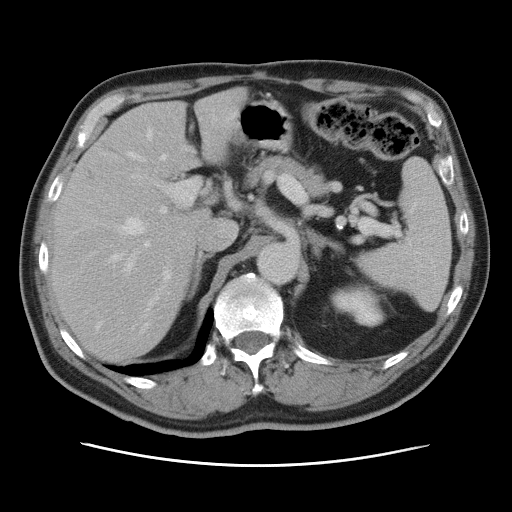
Contrast-enhanced abdominal CT, one axial slice. Position 51 of 80 along the scan axis. 120 kVp. Intravenous contrast given. Soft-tissue window (W 400 / L 40 HU). 512 × 512 image matrix, field of view 370 × 370 mm. Male patient, age 69 years. From the clinical record (not read from this slice): diagnosis: colorectal cancer liver metastases, imaged before liver resection.
Annotated regions visible in this slice (expert manual segmentation):
- hepatic veins: box from (x=96, y=130) to (x=168, y=331) px
- liver: (x=51, y=91)–(x=243, y=362)
- planned liver remnant (the part of the liver to remain after resection): (x=51, y=91)–(x=243, y=361)
- portal vein (with intrahepatic branches): (x=108, y=119)–(x=219, y=311)